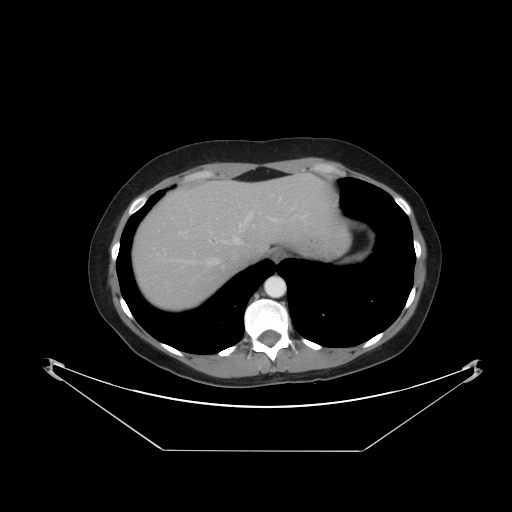
Contrast-enhanced abdominal CT, one axial slice; slice 39 of 48 in the series (ordered by position); 120 kVp; intravenous contrast given; soft-tissue window (W 400 / L 40 HU); 5 mm slice thickness; 512 × 512 image matrix, field of view 482 × 482 mm. Female patient, age 38 years. Case-level facts recorded for this patient, not image findings: diagnosis: colorectal cancer liver metastases, imaged before liver resection; multiple liver metastases: yes; largest metastasis: 2.5 cm; disease in both lobes: no.
Structures marked on this image (expert manual segmentation):
- hepatic veins: bounding box <182,200,310,266> (left, top, right, bottom; pixels)
- liver: <133,176,336,312>
- planned liver remnant (the part of the liver to remain after resection): <204,176,336,257>
- portal vein (with intrahepatic branches): <179,218,278,234>